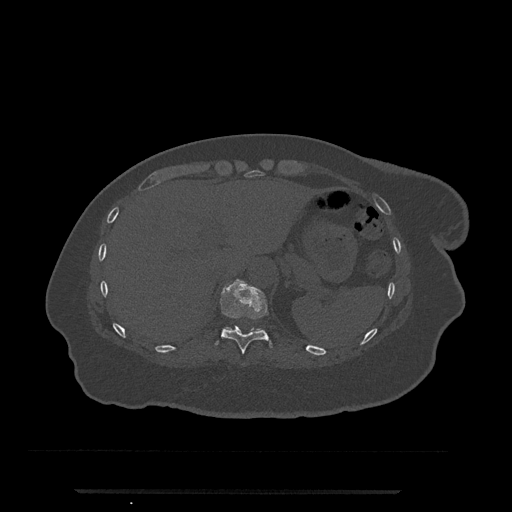
CT including the spine, one axial slice. Position 274 of 797 along the scan axis. 120 kVp. Bone window (W 1800 / L 400 HU). 512 × 512 image matrix. Female patient, age 51 years. From the clinical record (not read from this slice): primary cancer: neuro.
Annotated regions visible in this slice (semi-automatic segmentation, software-assisted and operator-edited):
- T10 vertebra: bounding box <214,279,273,354> (left, top, right, bottom; pixels)
- T11 vertebra: <227,327,231,330>